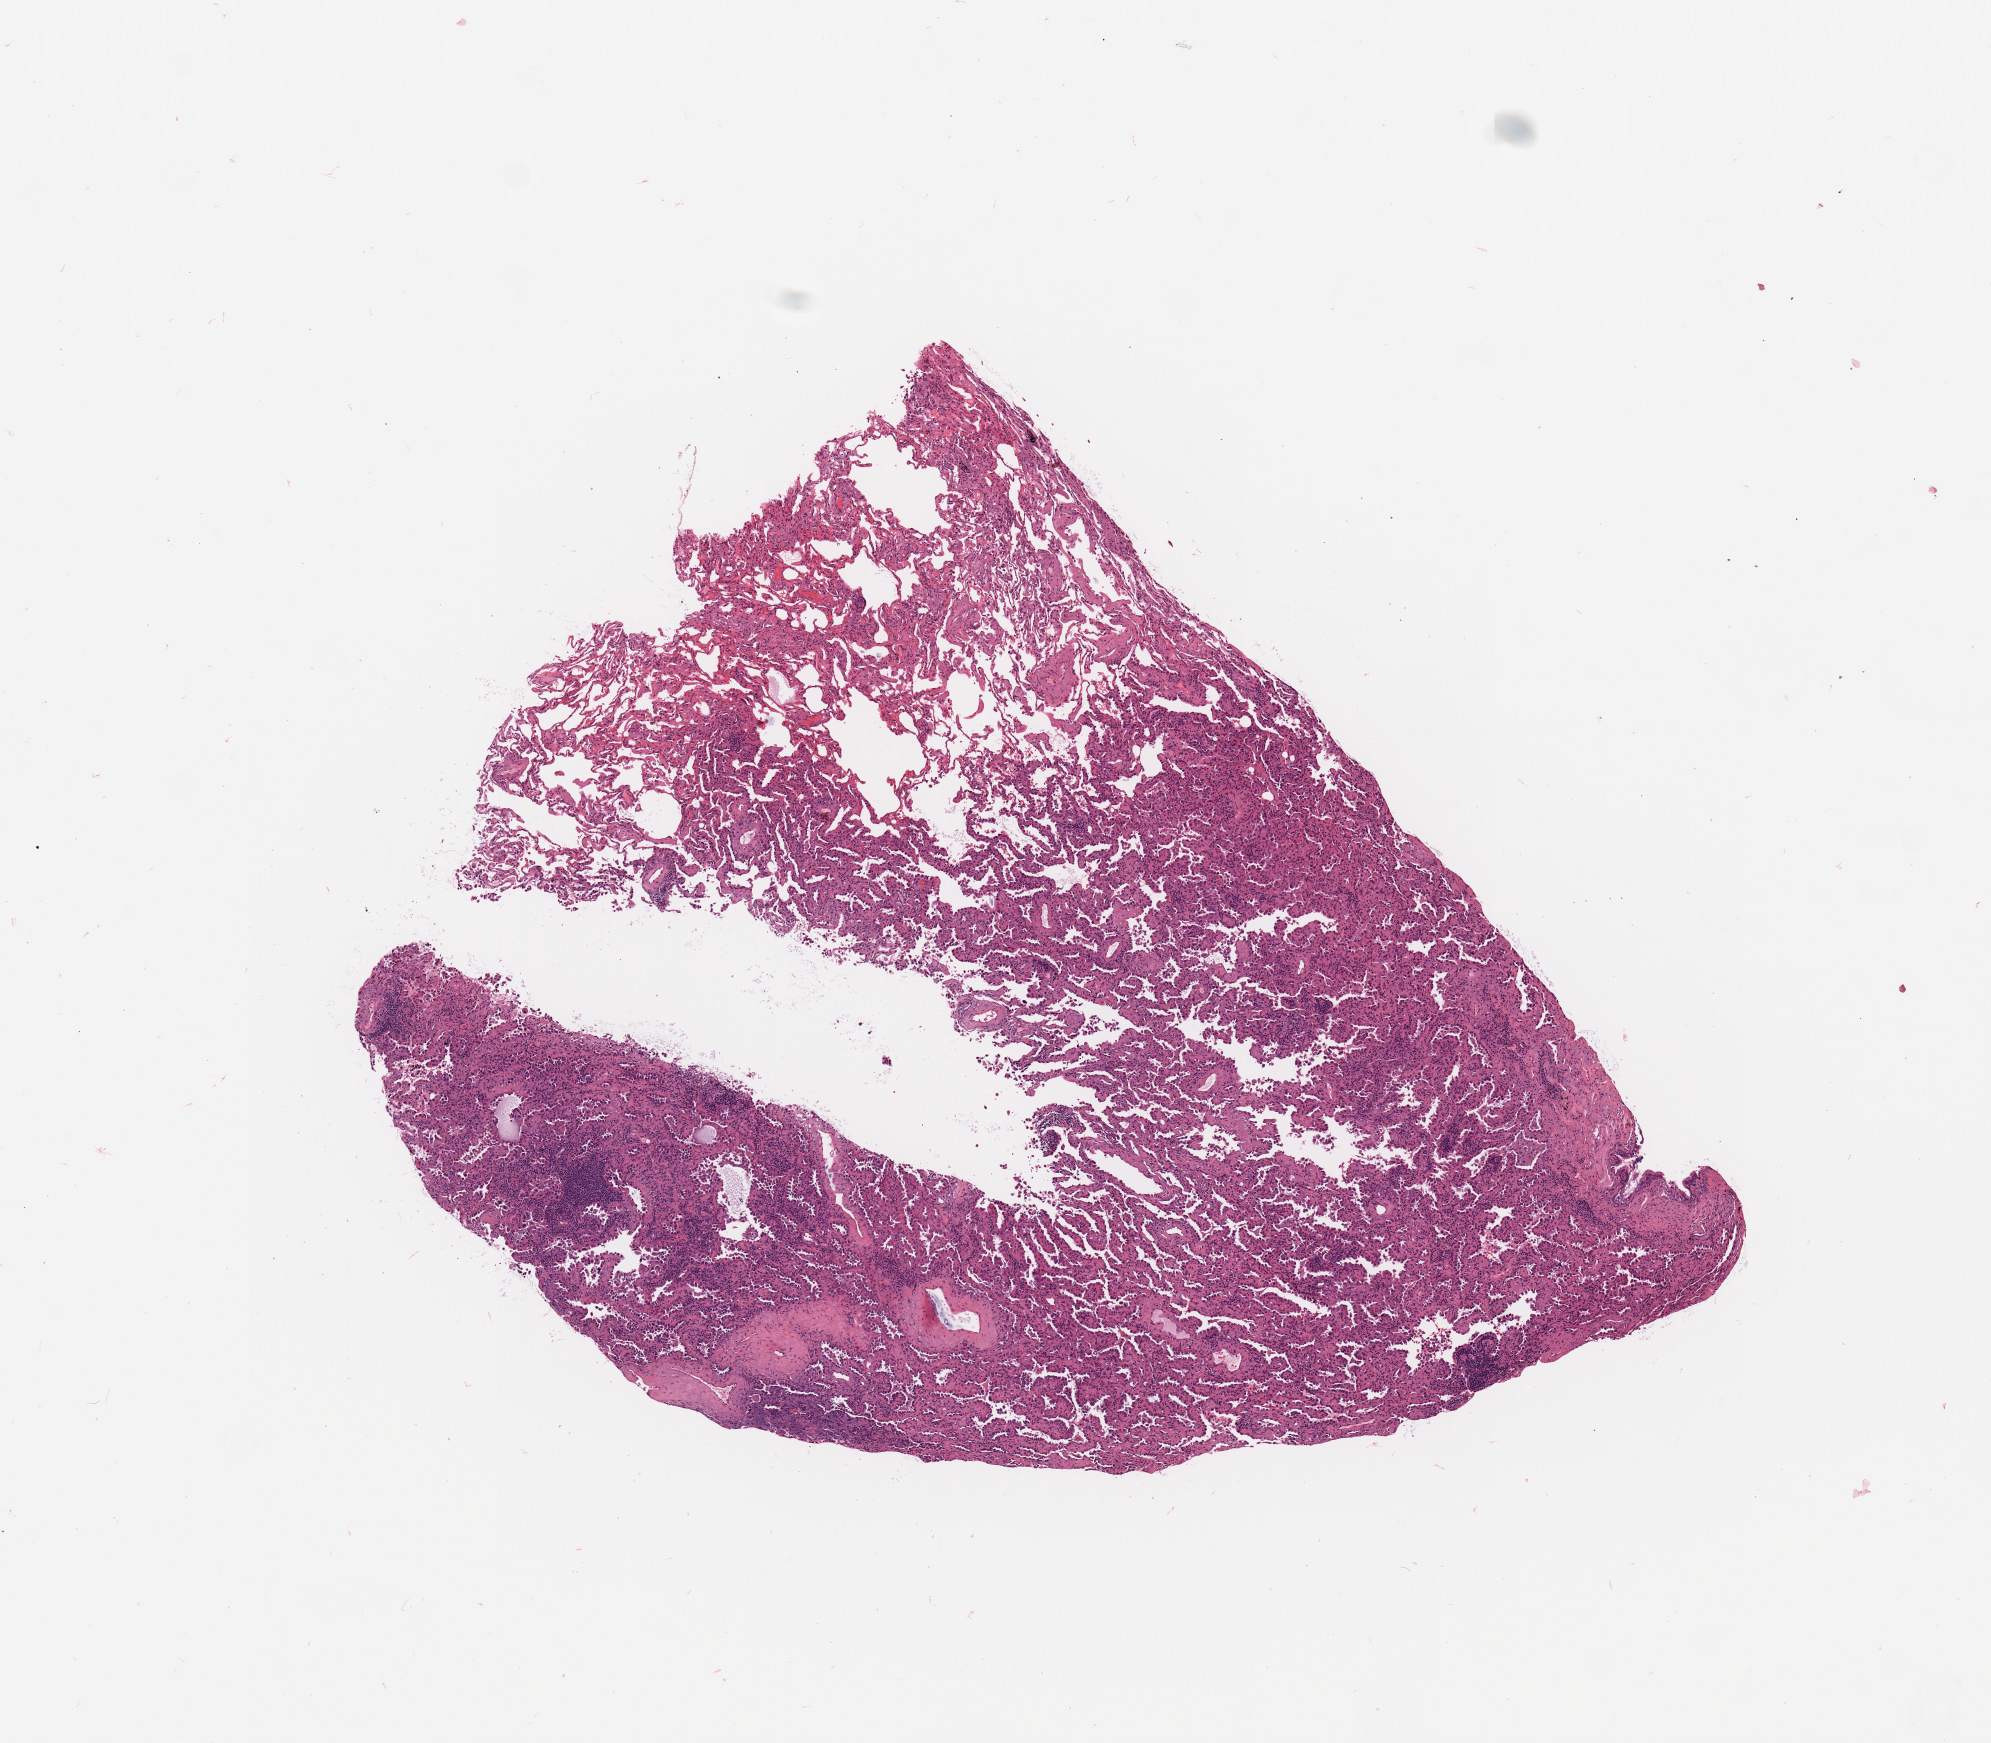
Digitized H&E-stained tissue section (whole slide), shown as a low-resolution overview of the whole scanned area (about 7.9 x 6.9 mm, slide scanned at 20x), tumour tissue sample, lung. Female, 70 y/o.
Histologic diagnosis: Adenocarcinoma, NOS.